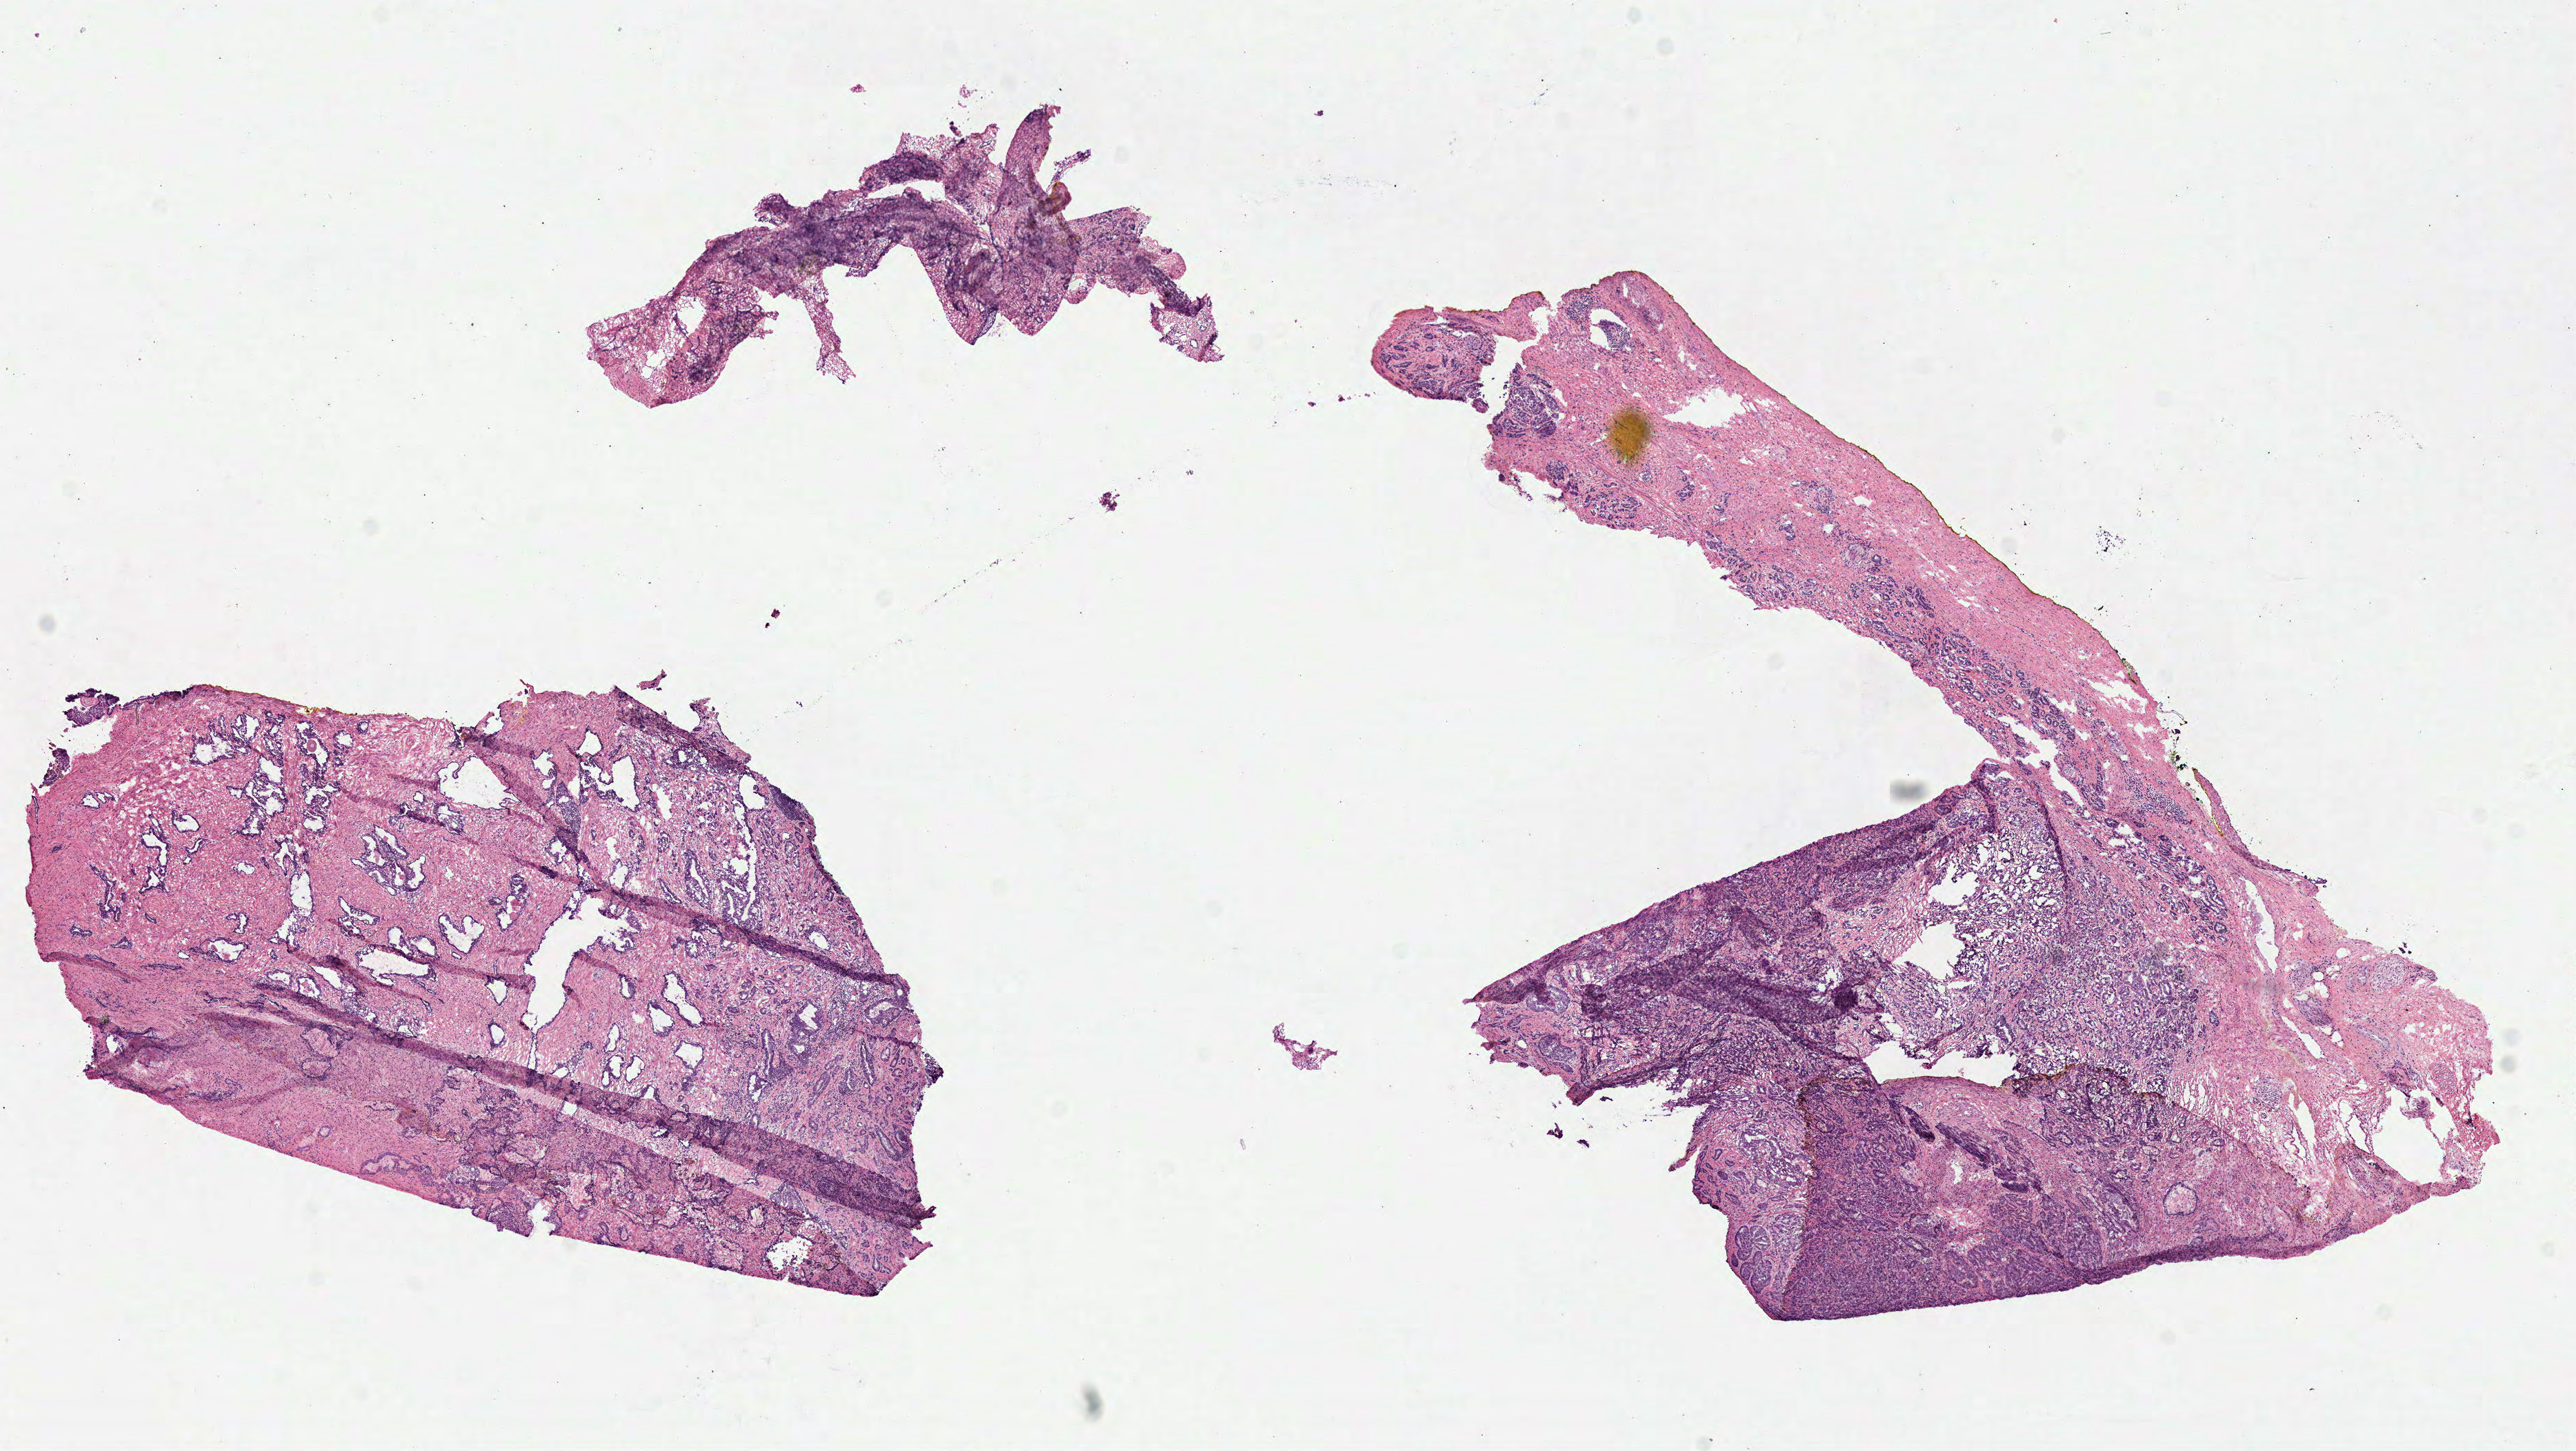
Digitized H&E tissue section (whole slide) — whole scanned area (about 14.7 x 8.3 mm, from a 40x scan) shown as a low-resolution overview; frozen section; prostate, primary tumour sample. Patient: male, age at initial diagnosis 68 years. Gleason score: 7 (4+3). Pathologist review of this section (percent, as recorded): tumour cells 60%, tumour nuclei 60%, normal cells 20%, stromal cells 20%, necrosis 0%. Infiltration values recorded for this section: lymphocyte infiltration 3%, monocyte infiltration 0%, neutrophil infiltration 0%.
Laterality: bilateral. Pathologic diagnosis: Acinar cell carcinoma (prostate gland).